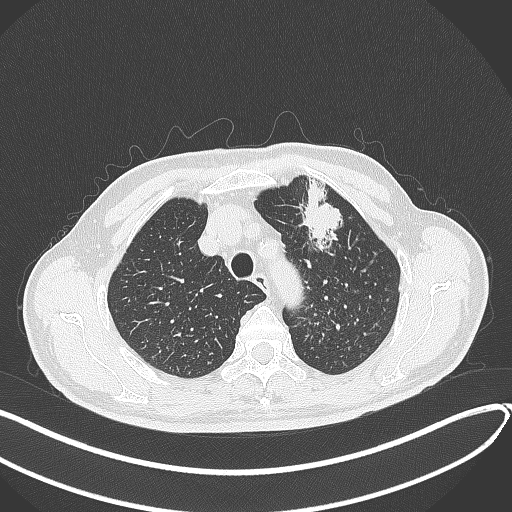
Chest CT, one axial slice. Position 338 of 459 along the scan axis. Reconstruction kernel B70f. 120 kVp. Lung window (W 1500 / L -600 HU). 1 mm slice thickness. 512 × 512 image matrix. Male patient, age 74 years. From the clinical record (not read from this slice): clinical TNM (as recorded): T2b N0 M1c.
Structures marked on this image (bounding box drawn by a radiologist):
- lung tumour (recorded histology: adenocarcinoma): bounding box [x1, y1, x2, y2] px = [293, 172, 348, 258]